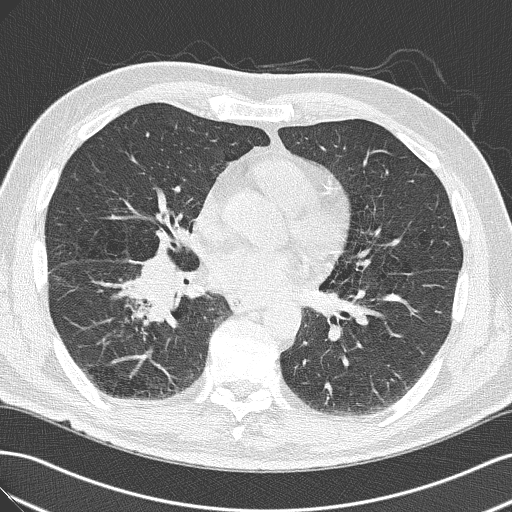
Low-dose screening chest CT, axial slice. First (baseline) screen. Lung window (W 1500 / L -600 HU). 2 mm slice thickness. Slice 86 of 143 in the series. 512 × 512 image matrix, field of view 360 × 360 mm. Male, age 65 years at enrolment.
Expert-annotated lung lesion, bounding box [x1, y1, x2, y2] px = [103, 253, 207, 340]. The exam's reader record, not a measurement of the box and not confirmed to be the same lesion: non-calcified nodule or mass ≥4 mm, right upper lobe, 18 × 13 mm, spiculated (stellate) margins, soft tissue attenuation. Official screen result: positive, change unspecified: nodule(s) >= 4 mm or enlarging nodule(s), mass(es), or other non-specific abnormalities suspicious for lung cancer.